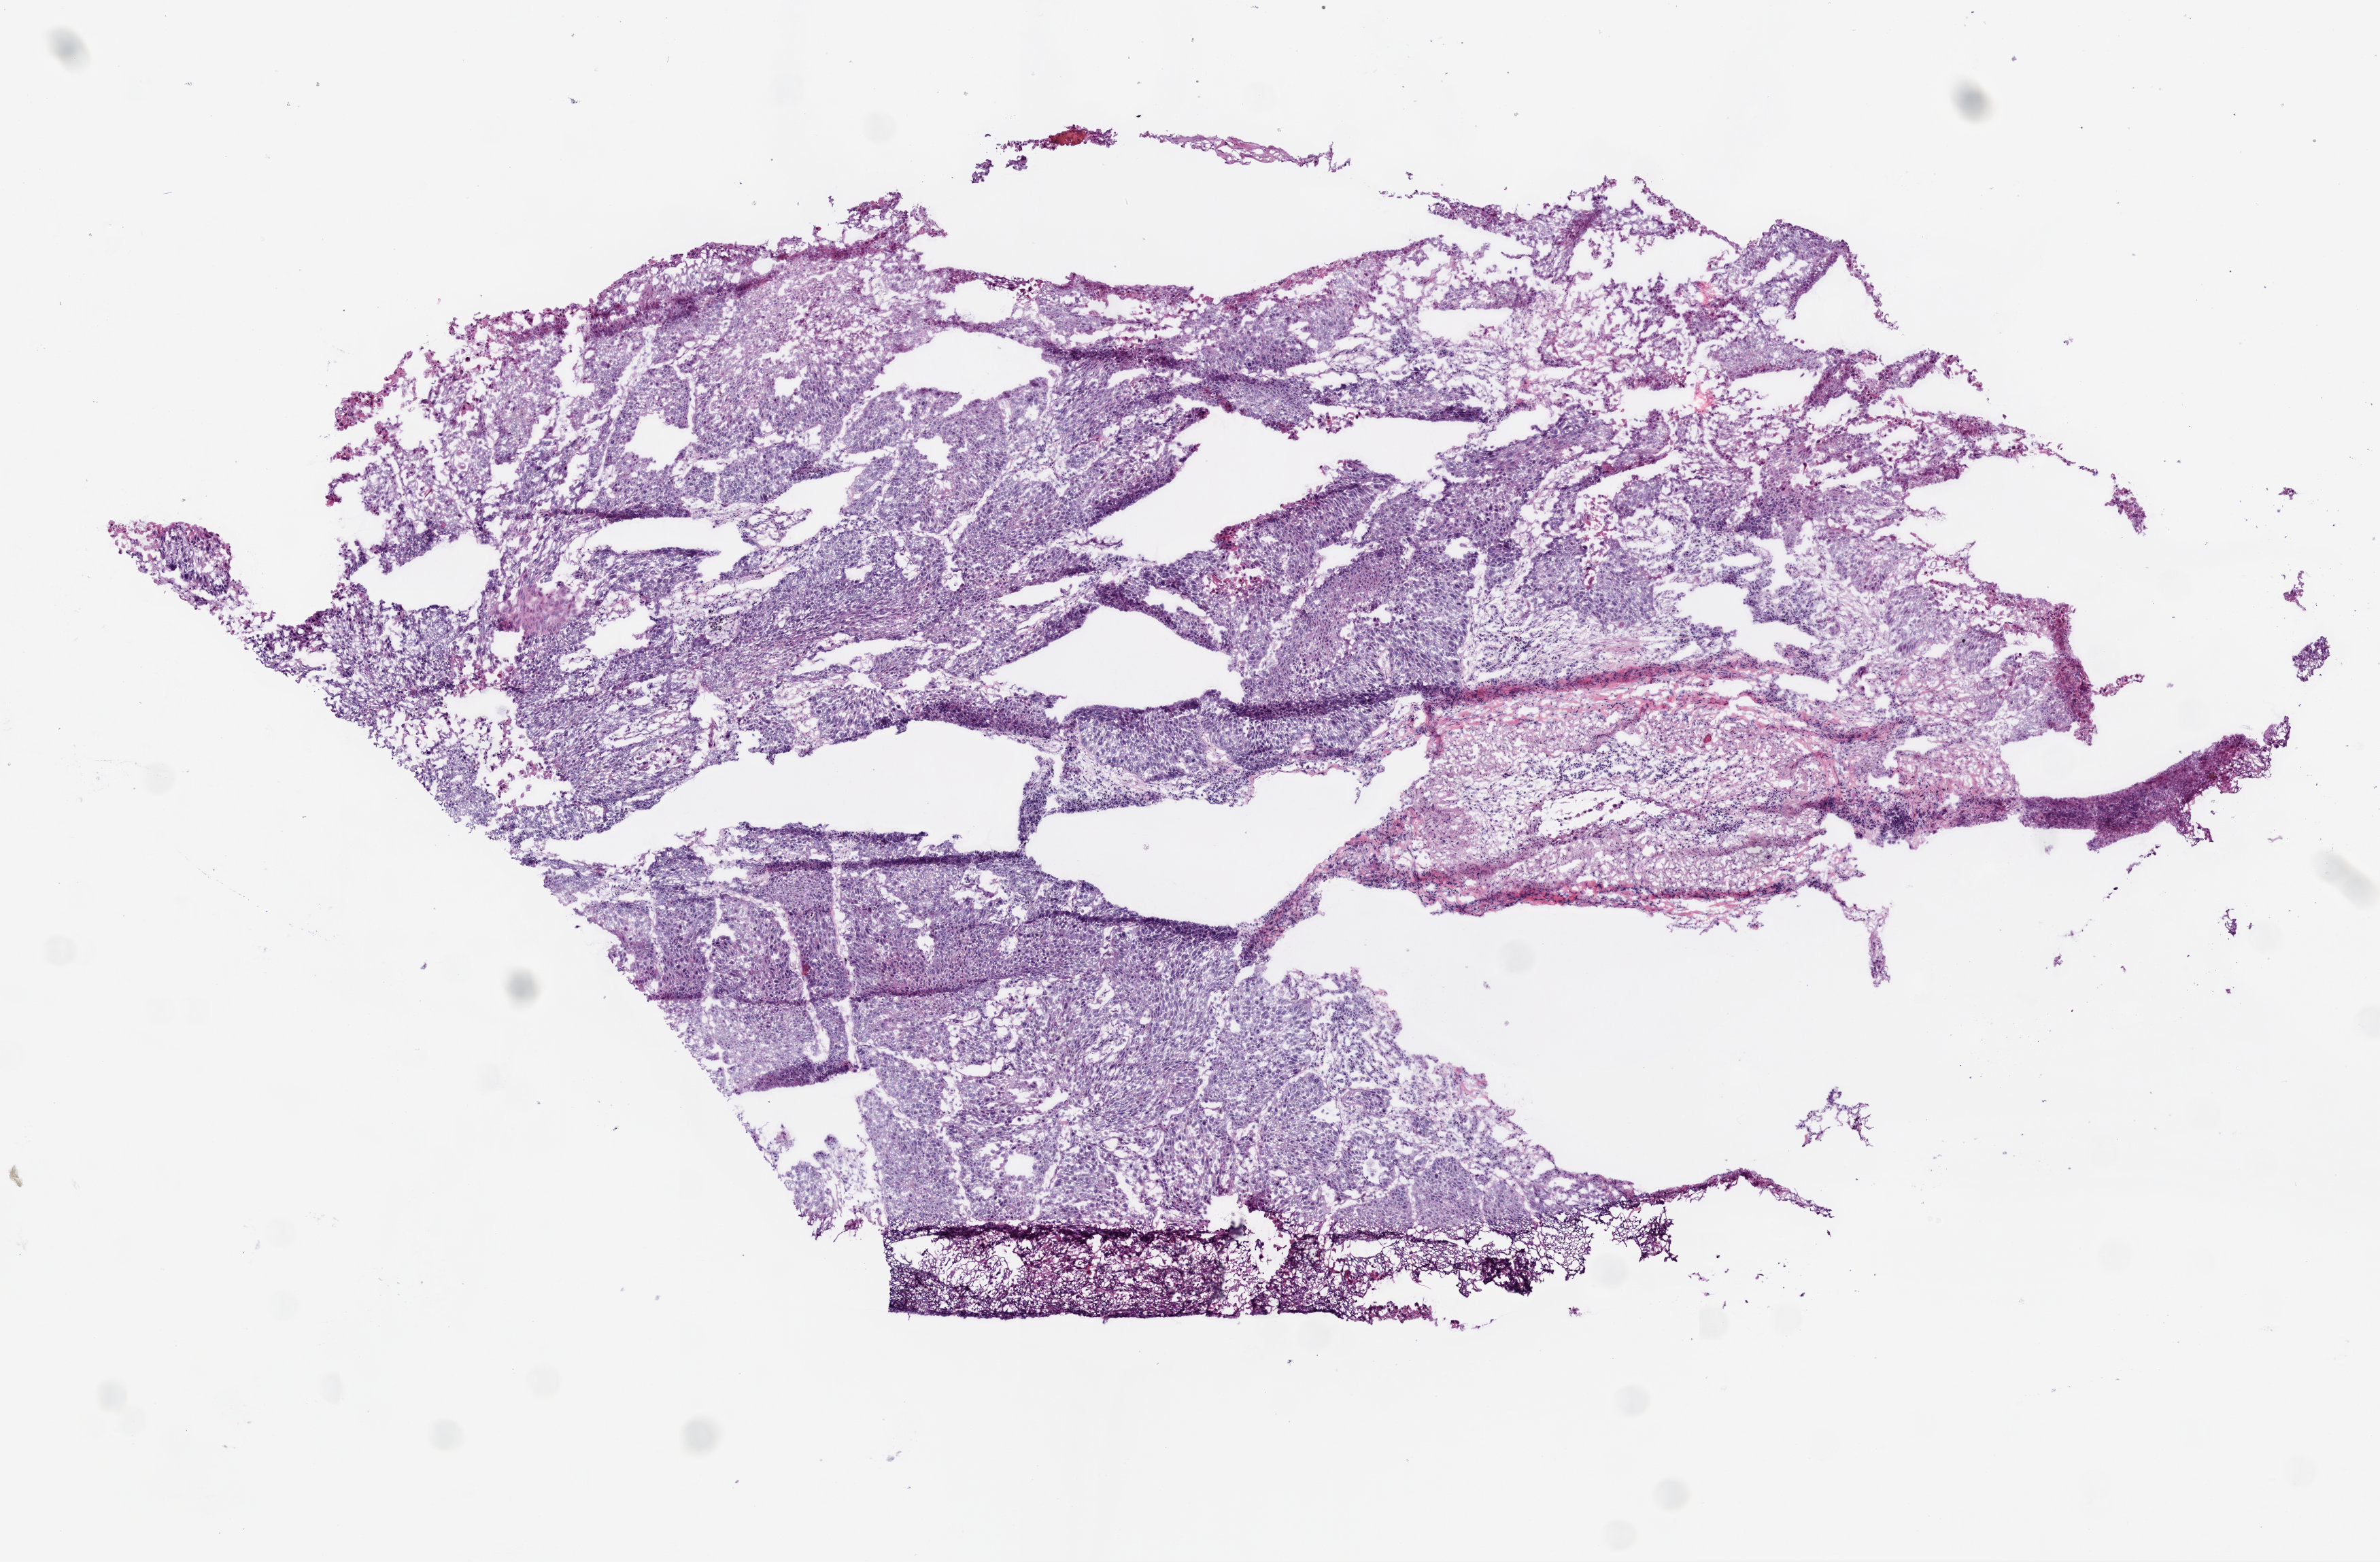
H&E whole-slide image, a low-resolution overview of the entire scanned area, about 7.0 x 4.6 mm (acquisition: 20x scan). Frozen section from the bottom of the tissue portion. Sample: primary tumour, lung. Male, age 52 years at initial diagnosis. Pathologist review of this section (percent, as recorded): tumour cells 80%, tumour nuclei 88%, normal cells 0%, stromal cells 12%, necrosis 8%. Inflammatory infiltration, as recorded: lymphocyte infiltration 2%.
AJCC pathologic stage: IB. Pathologic diagnosis: Squamous cell carcinoma, NOS (lower lobe, lung). Laterality: left.